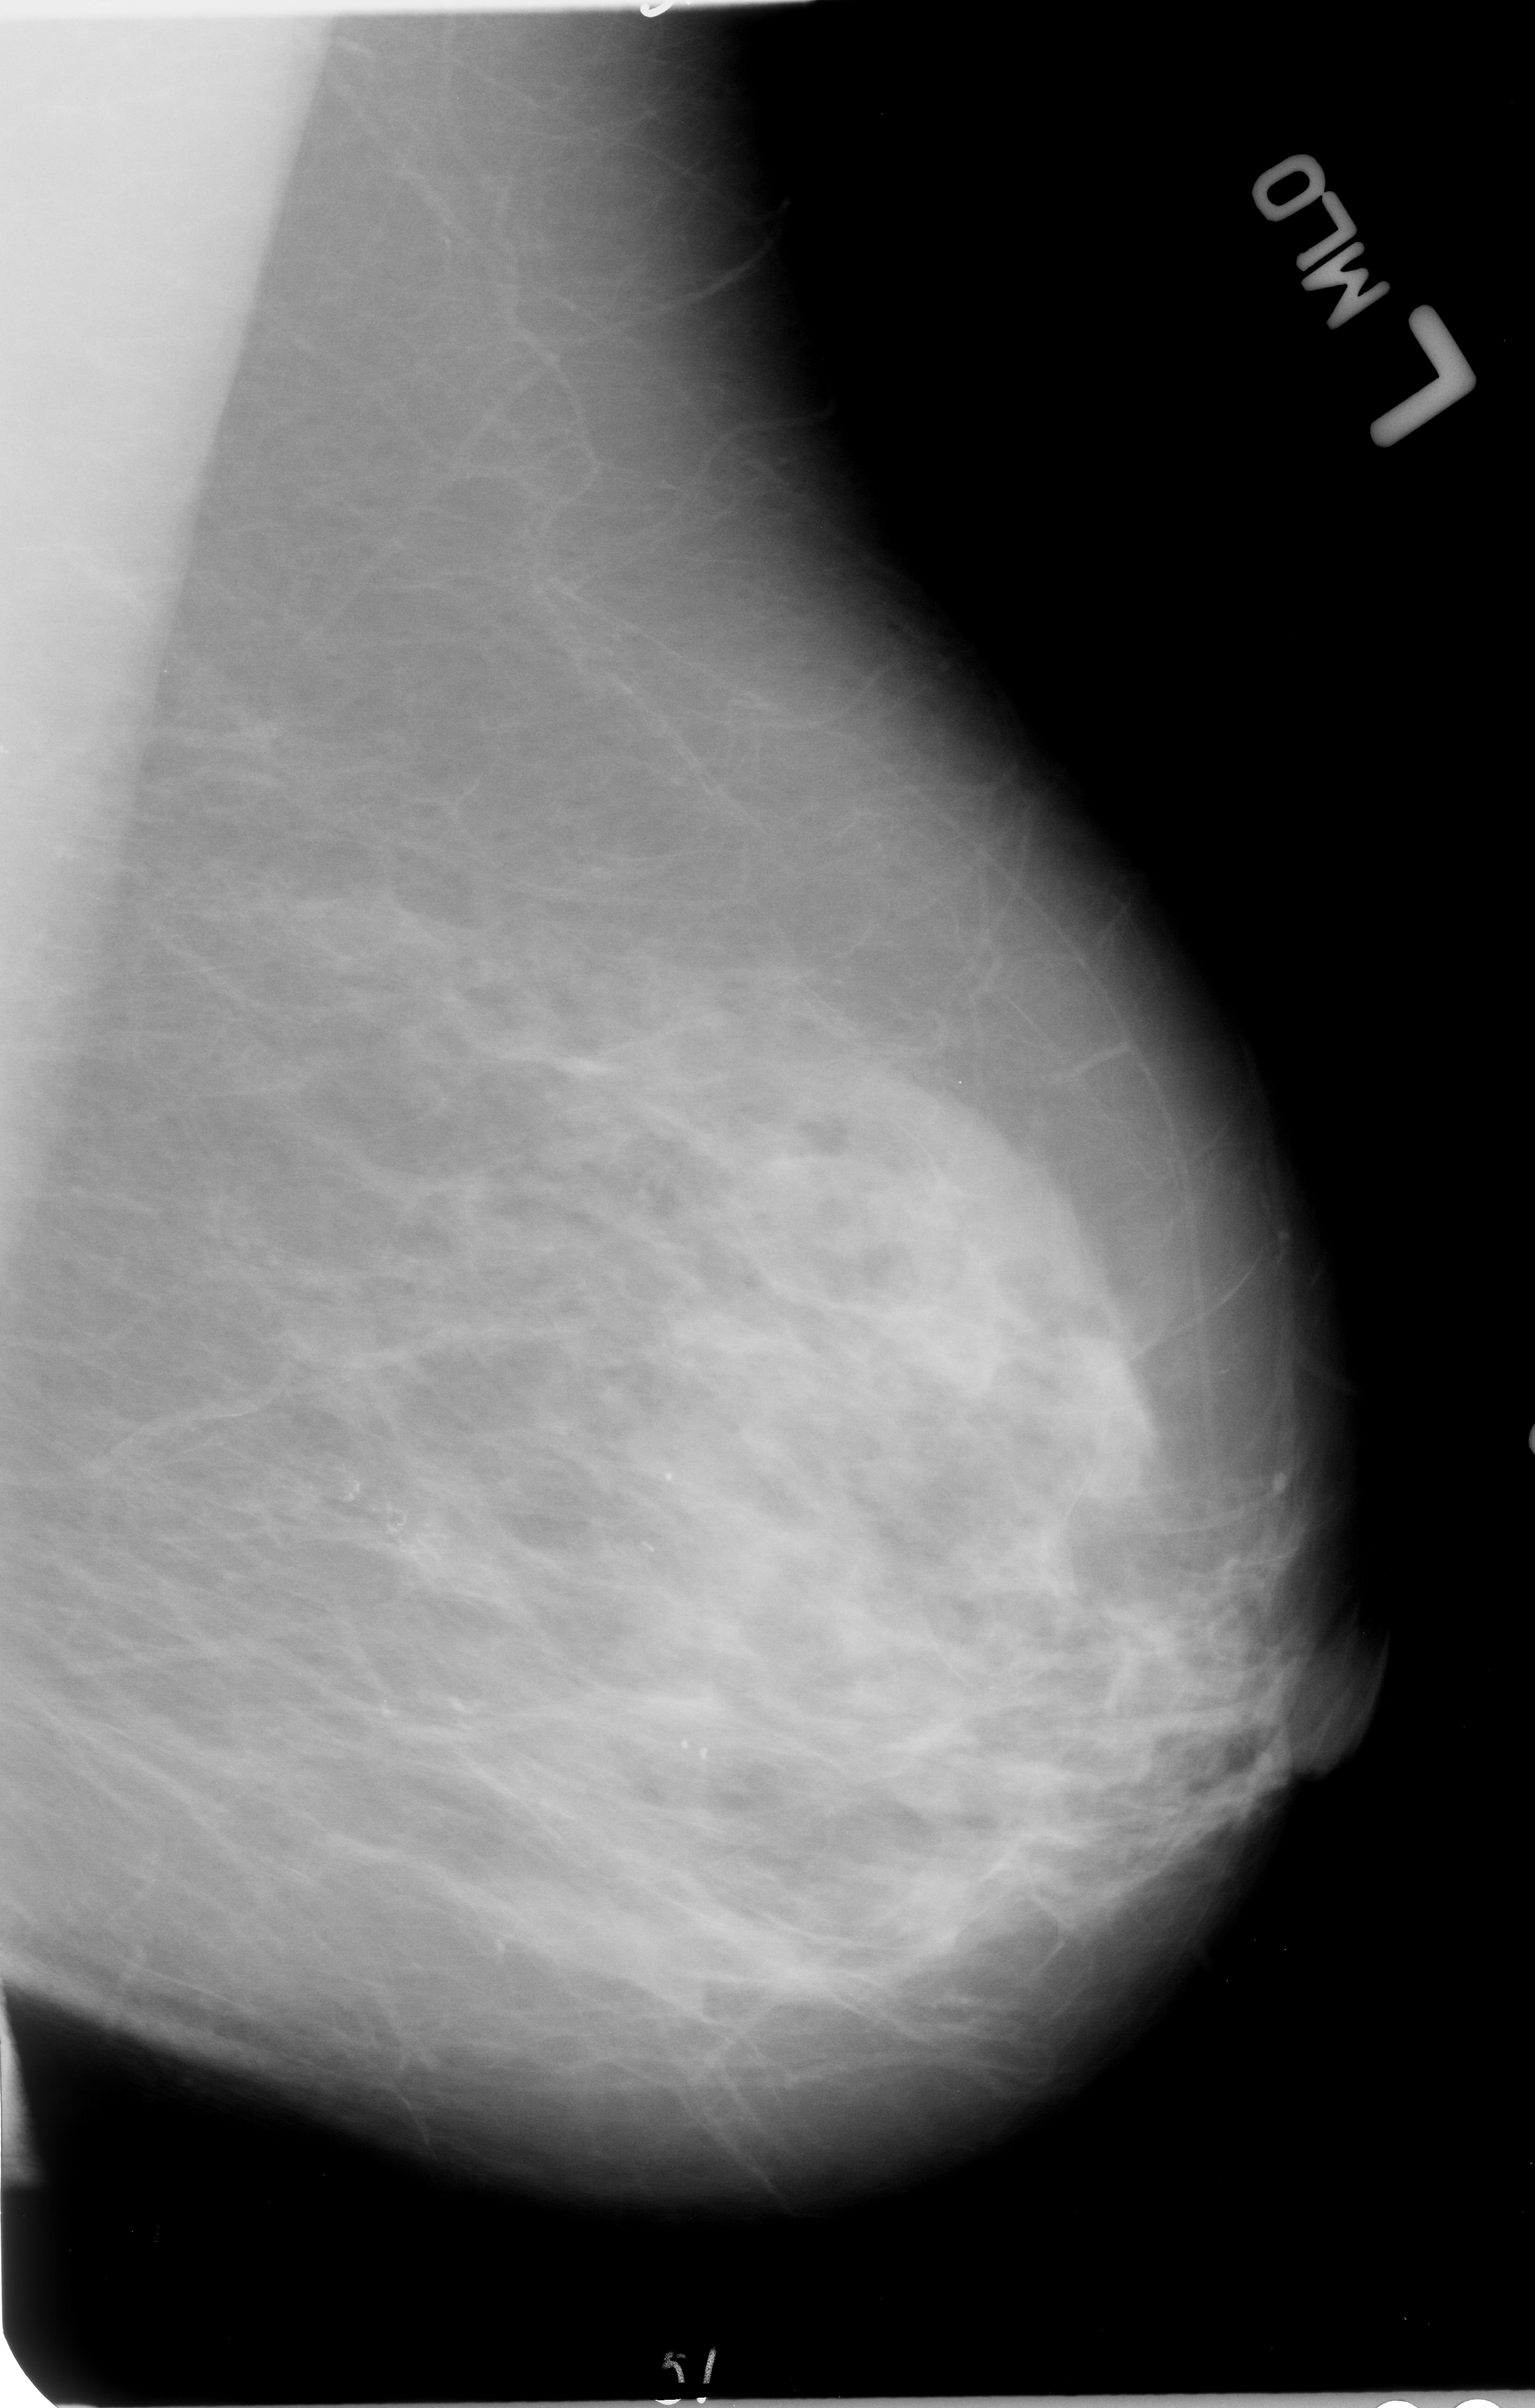
Mammogram (digitized film); left breast; MLO view; BI-RADS breast density category 3 (scale 1–4); 1535 × 2408 image matrix.
Expert-marked regions of interest on this image (one box per marked abnormality):
- calcifications, morphology pleomorphic / fine linear branching, distribution clustered / linear; BI-RADS assessment category 5; subtlety rating 4 on a 1 (subtle) to 5 (obvious) scale; pathology (as recorded): malignant: bounding box [x1, y1, x2, y2] px = [256, 1439, 469, 1602]